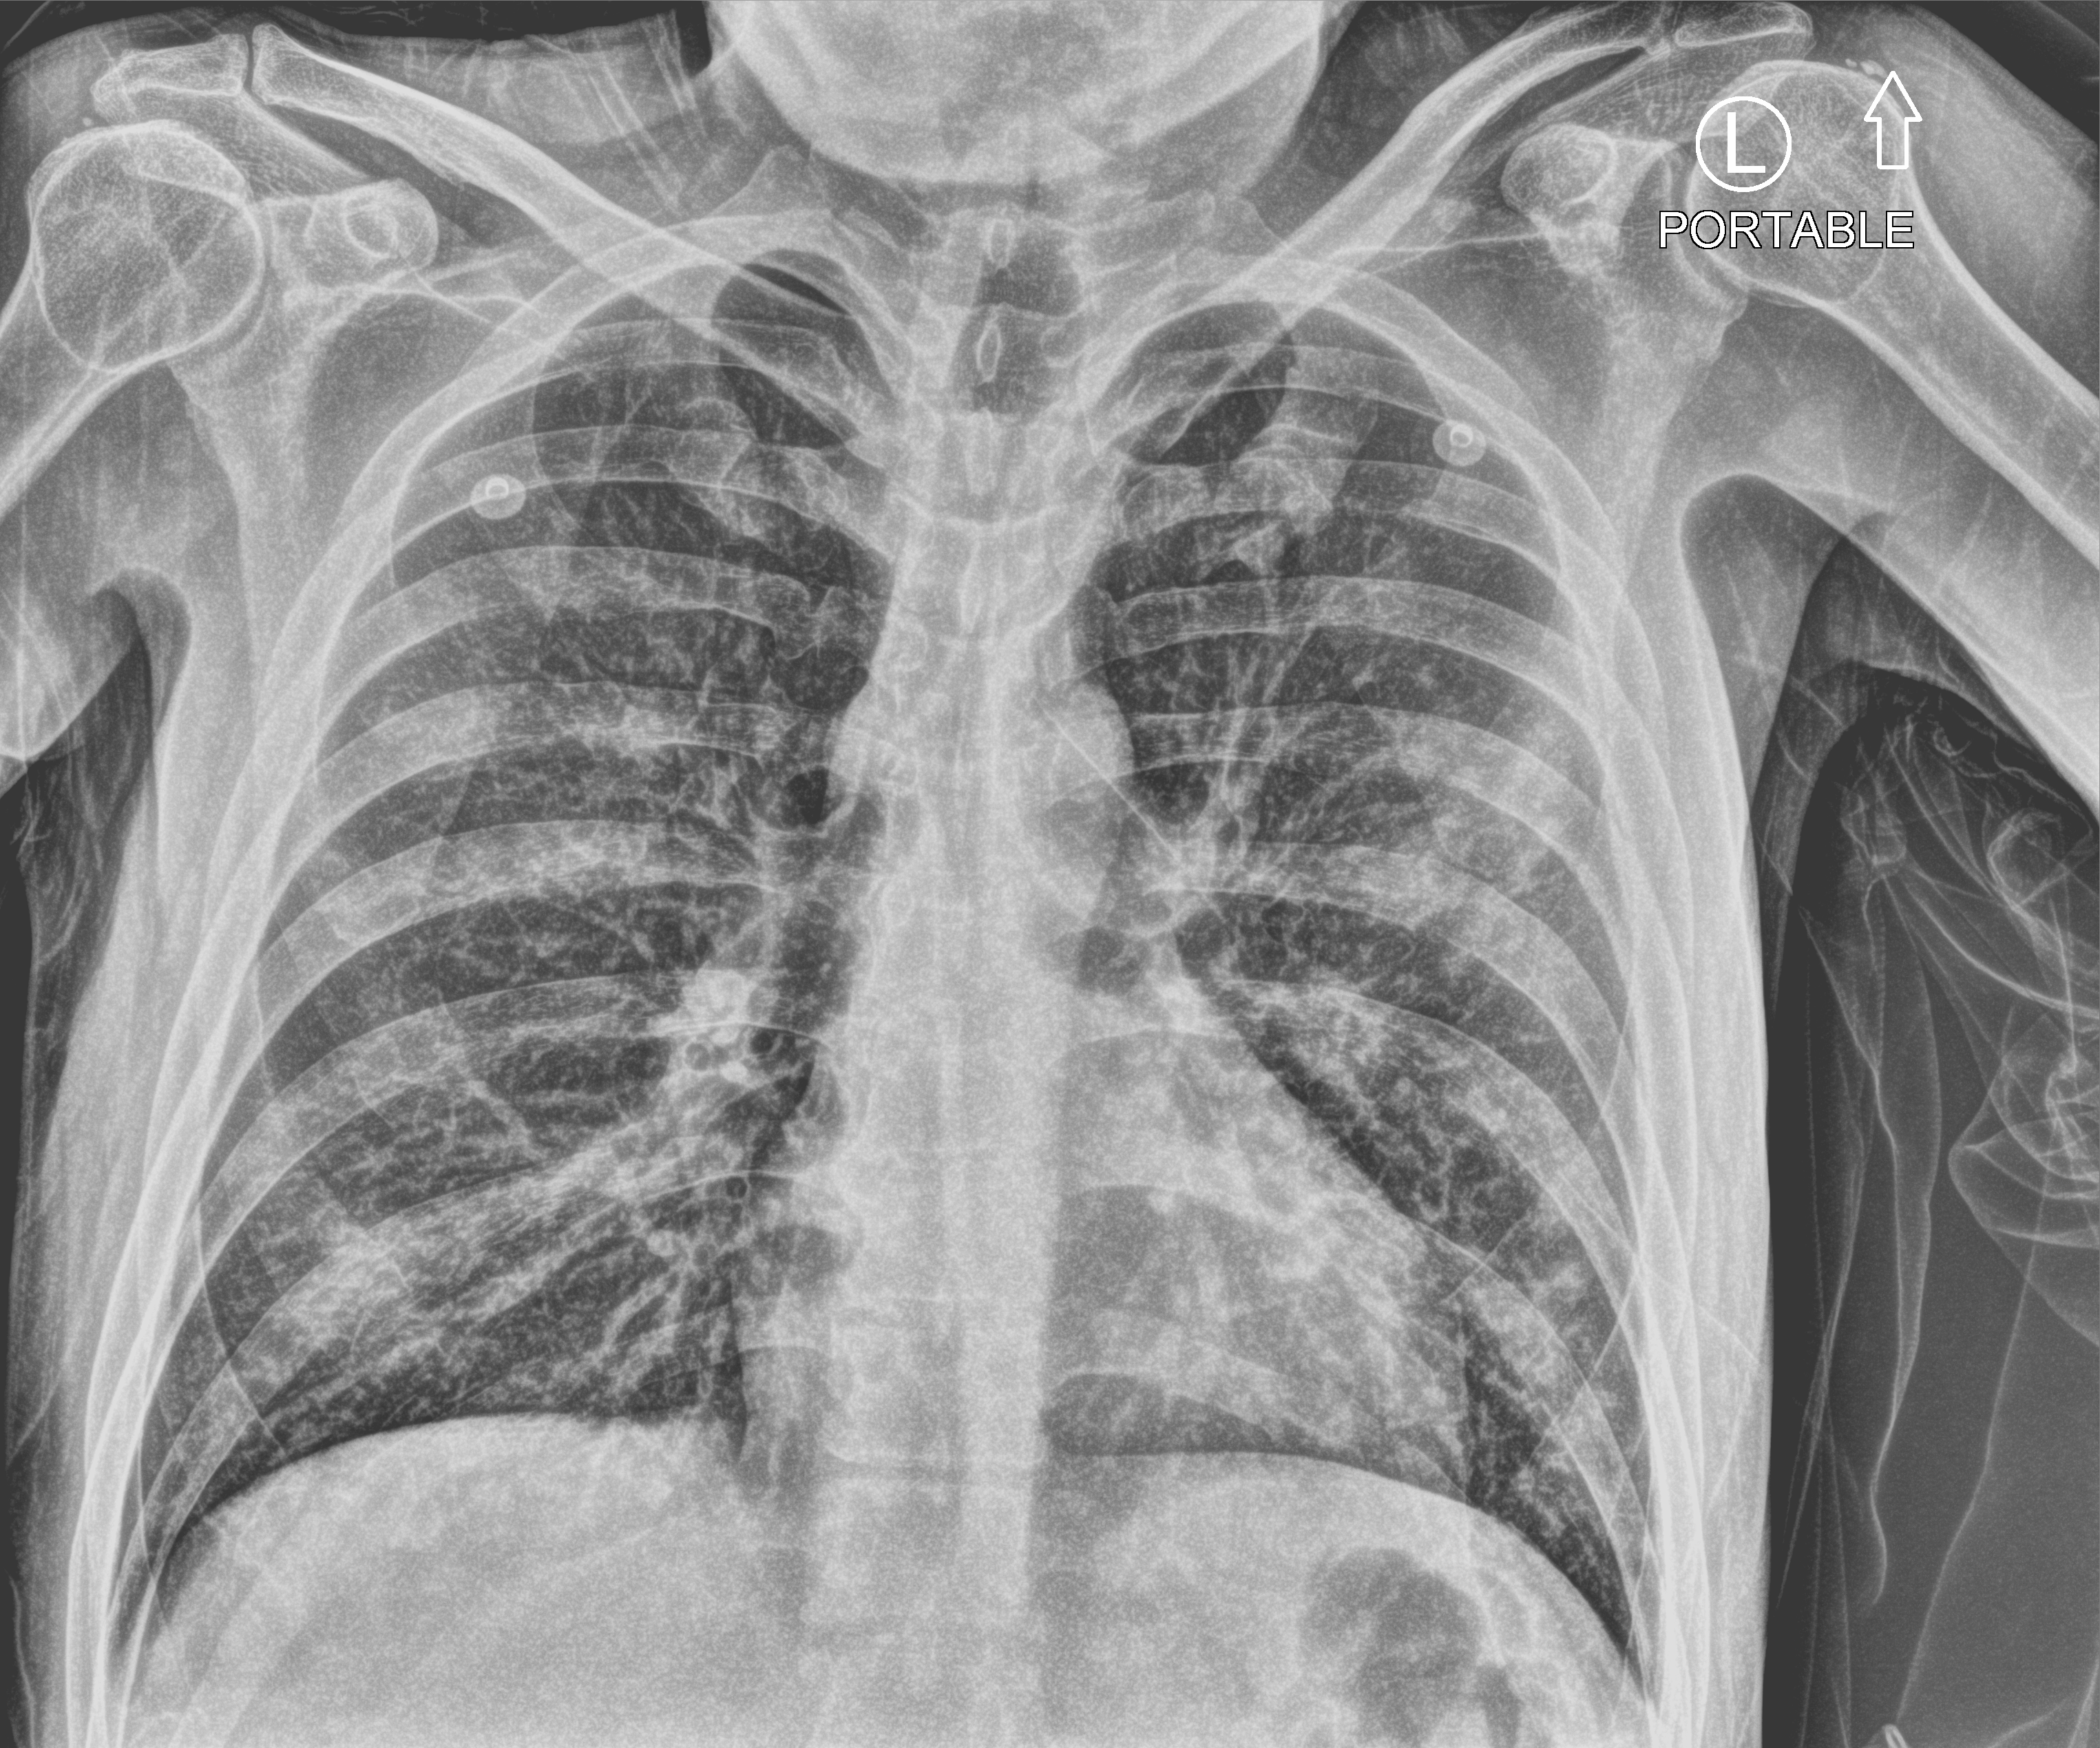
Bedside chest radiograph (computed radiography), anteroposterior (AP) projection. Patient hospitalised with COVID-19; male, aged 18–59 years.
Admission-level facts for this patient (not findings on this image; timing relative to this image not recorded): length of hospital stay: 1 day.